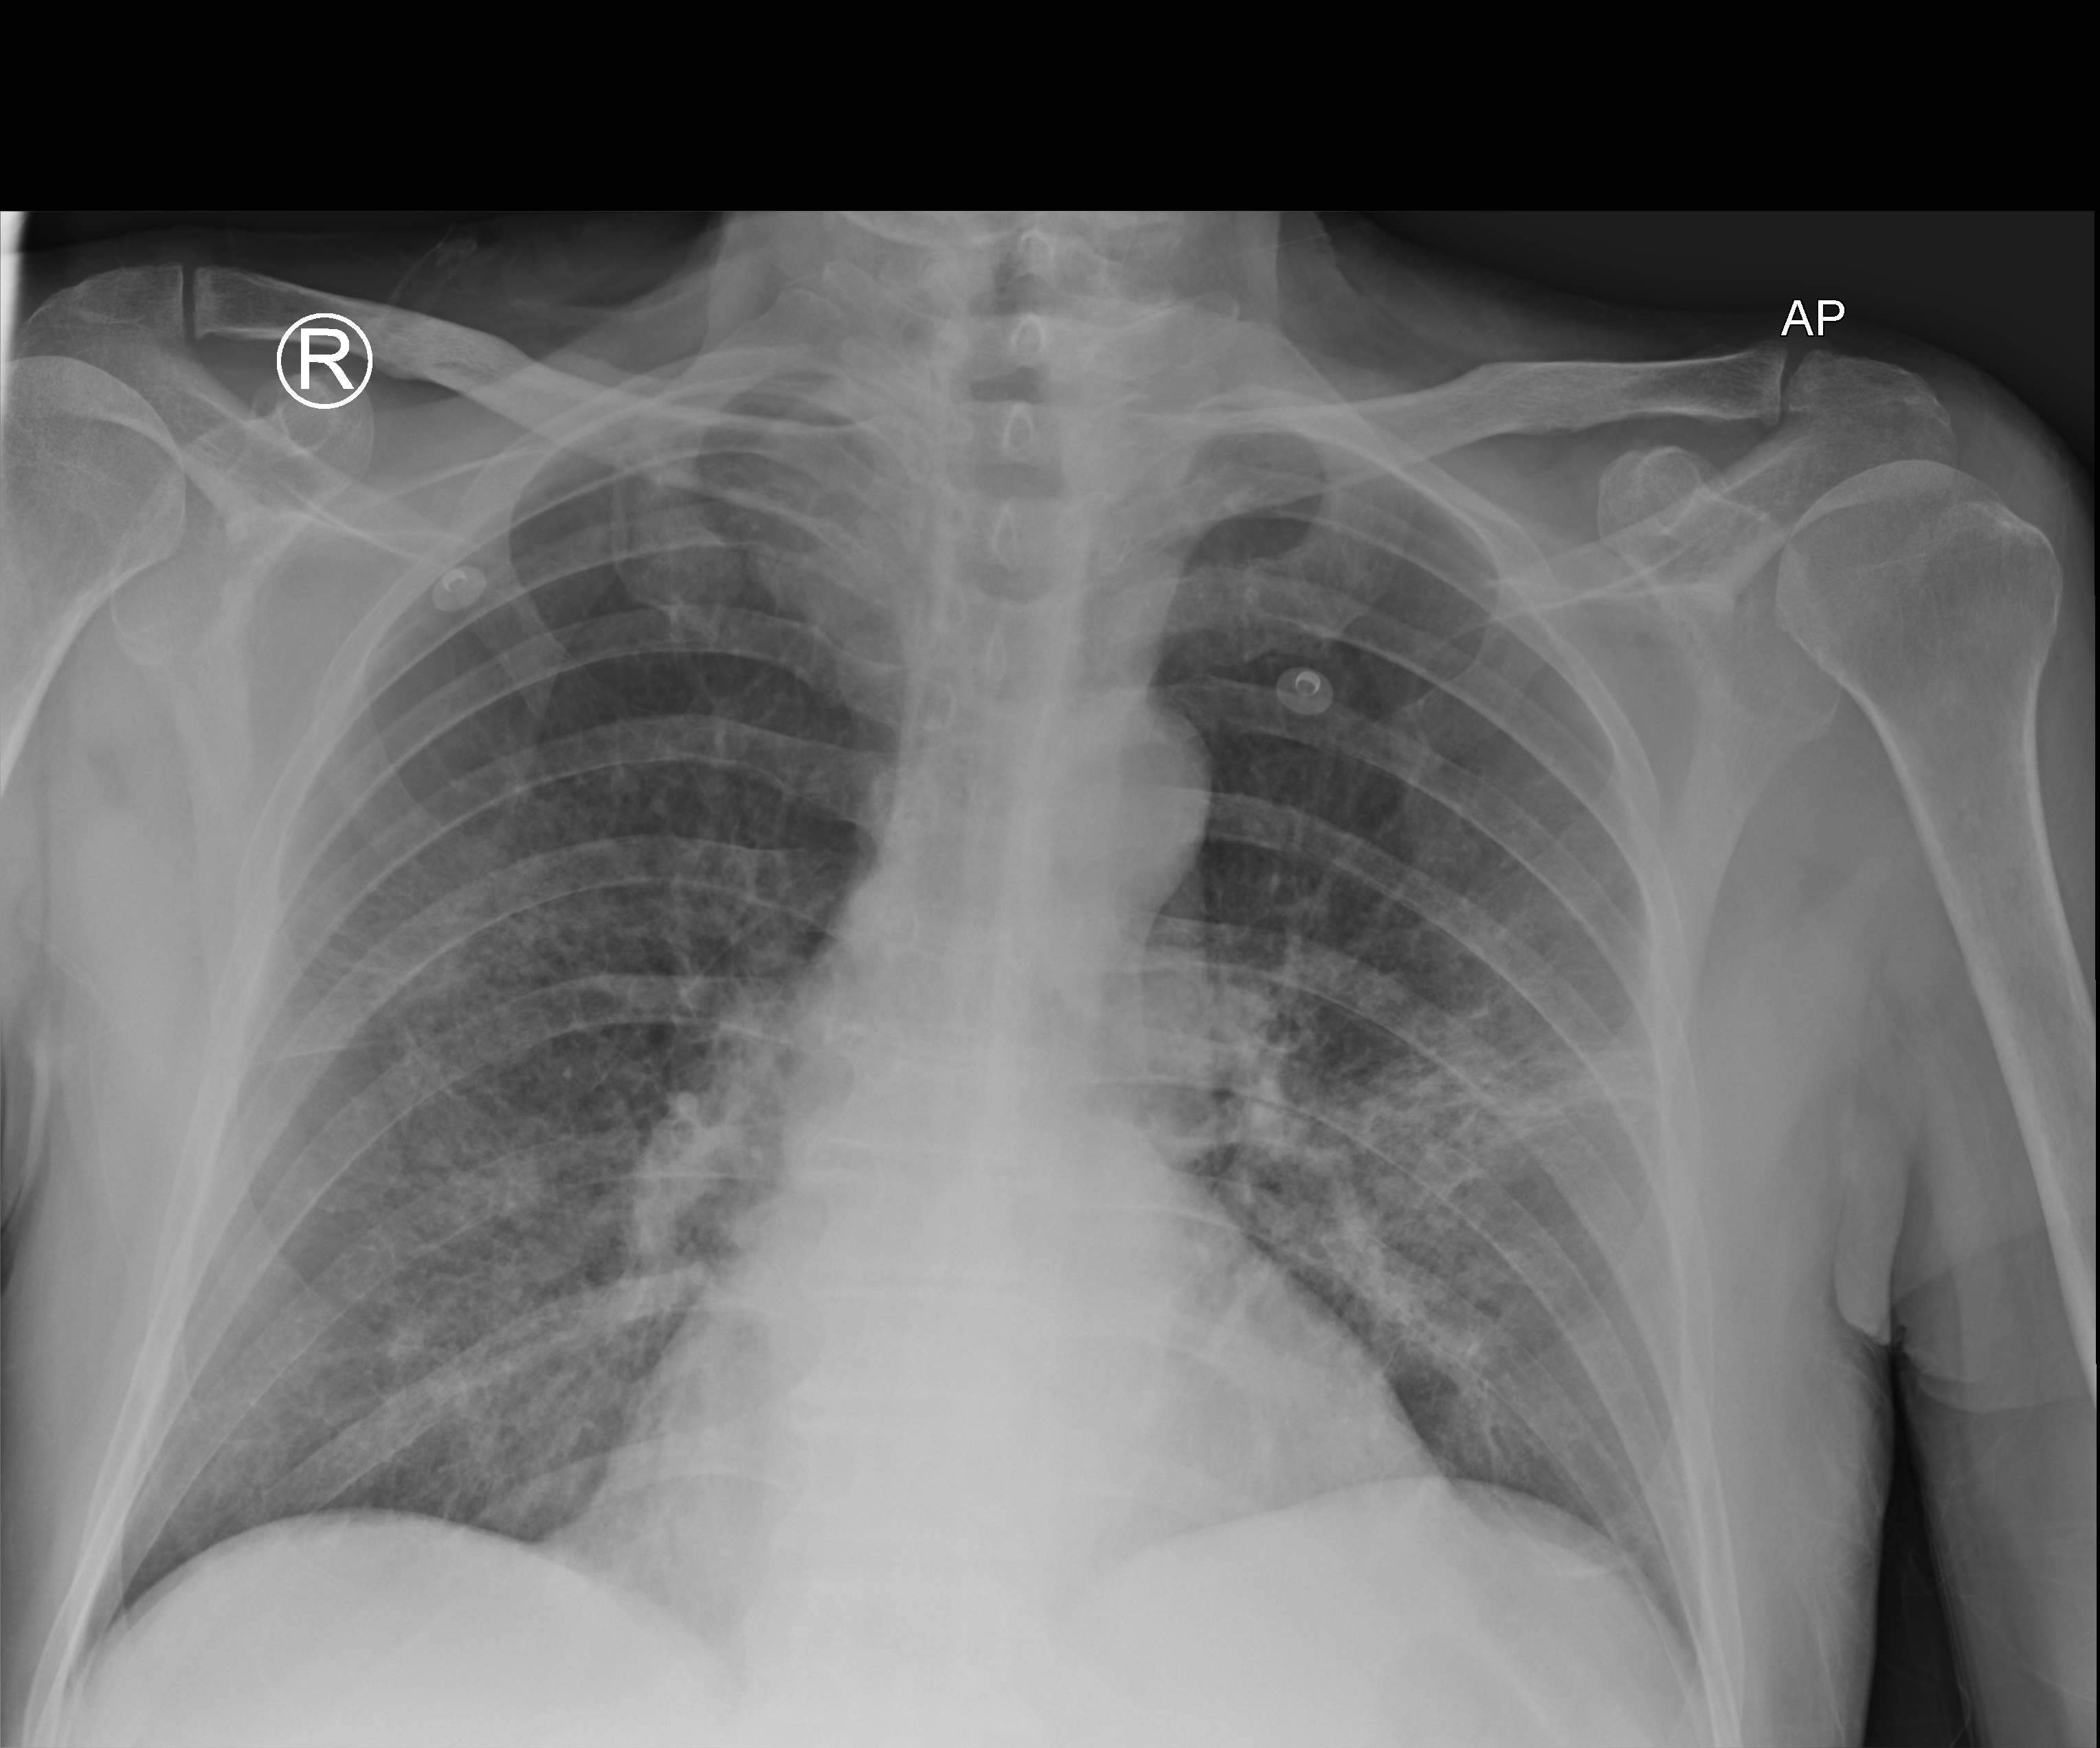
Chest radiograph (computed radiography); anteroposterior (AP) projection. Male patient hospitalised with COVID-19, age 75–90 years.
Hospital-stay facts (about this admission, not read from this image; timing relative to this image not recorded): mechanically ventilated during this hospital stay: no; admitted to intensive care during this hospital stay: no.